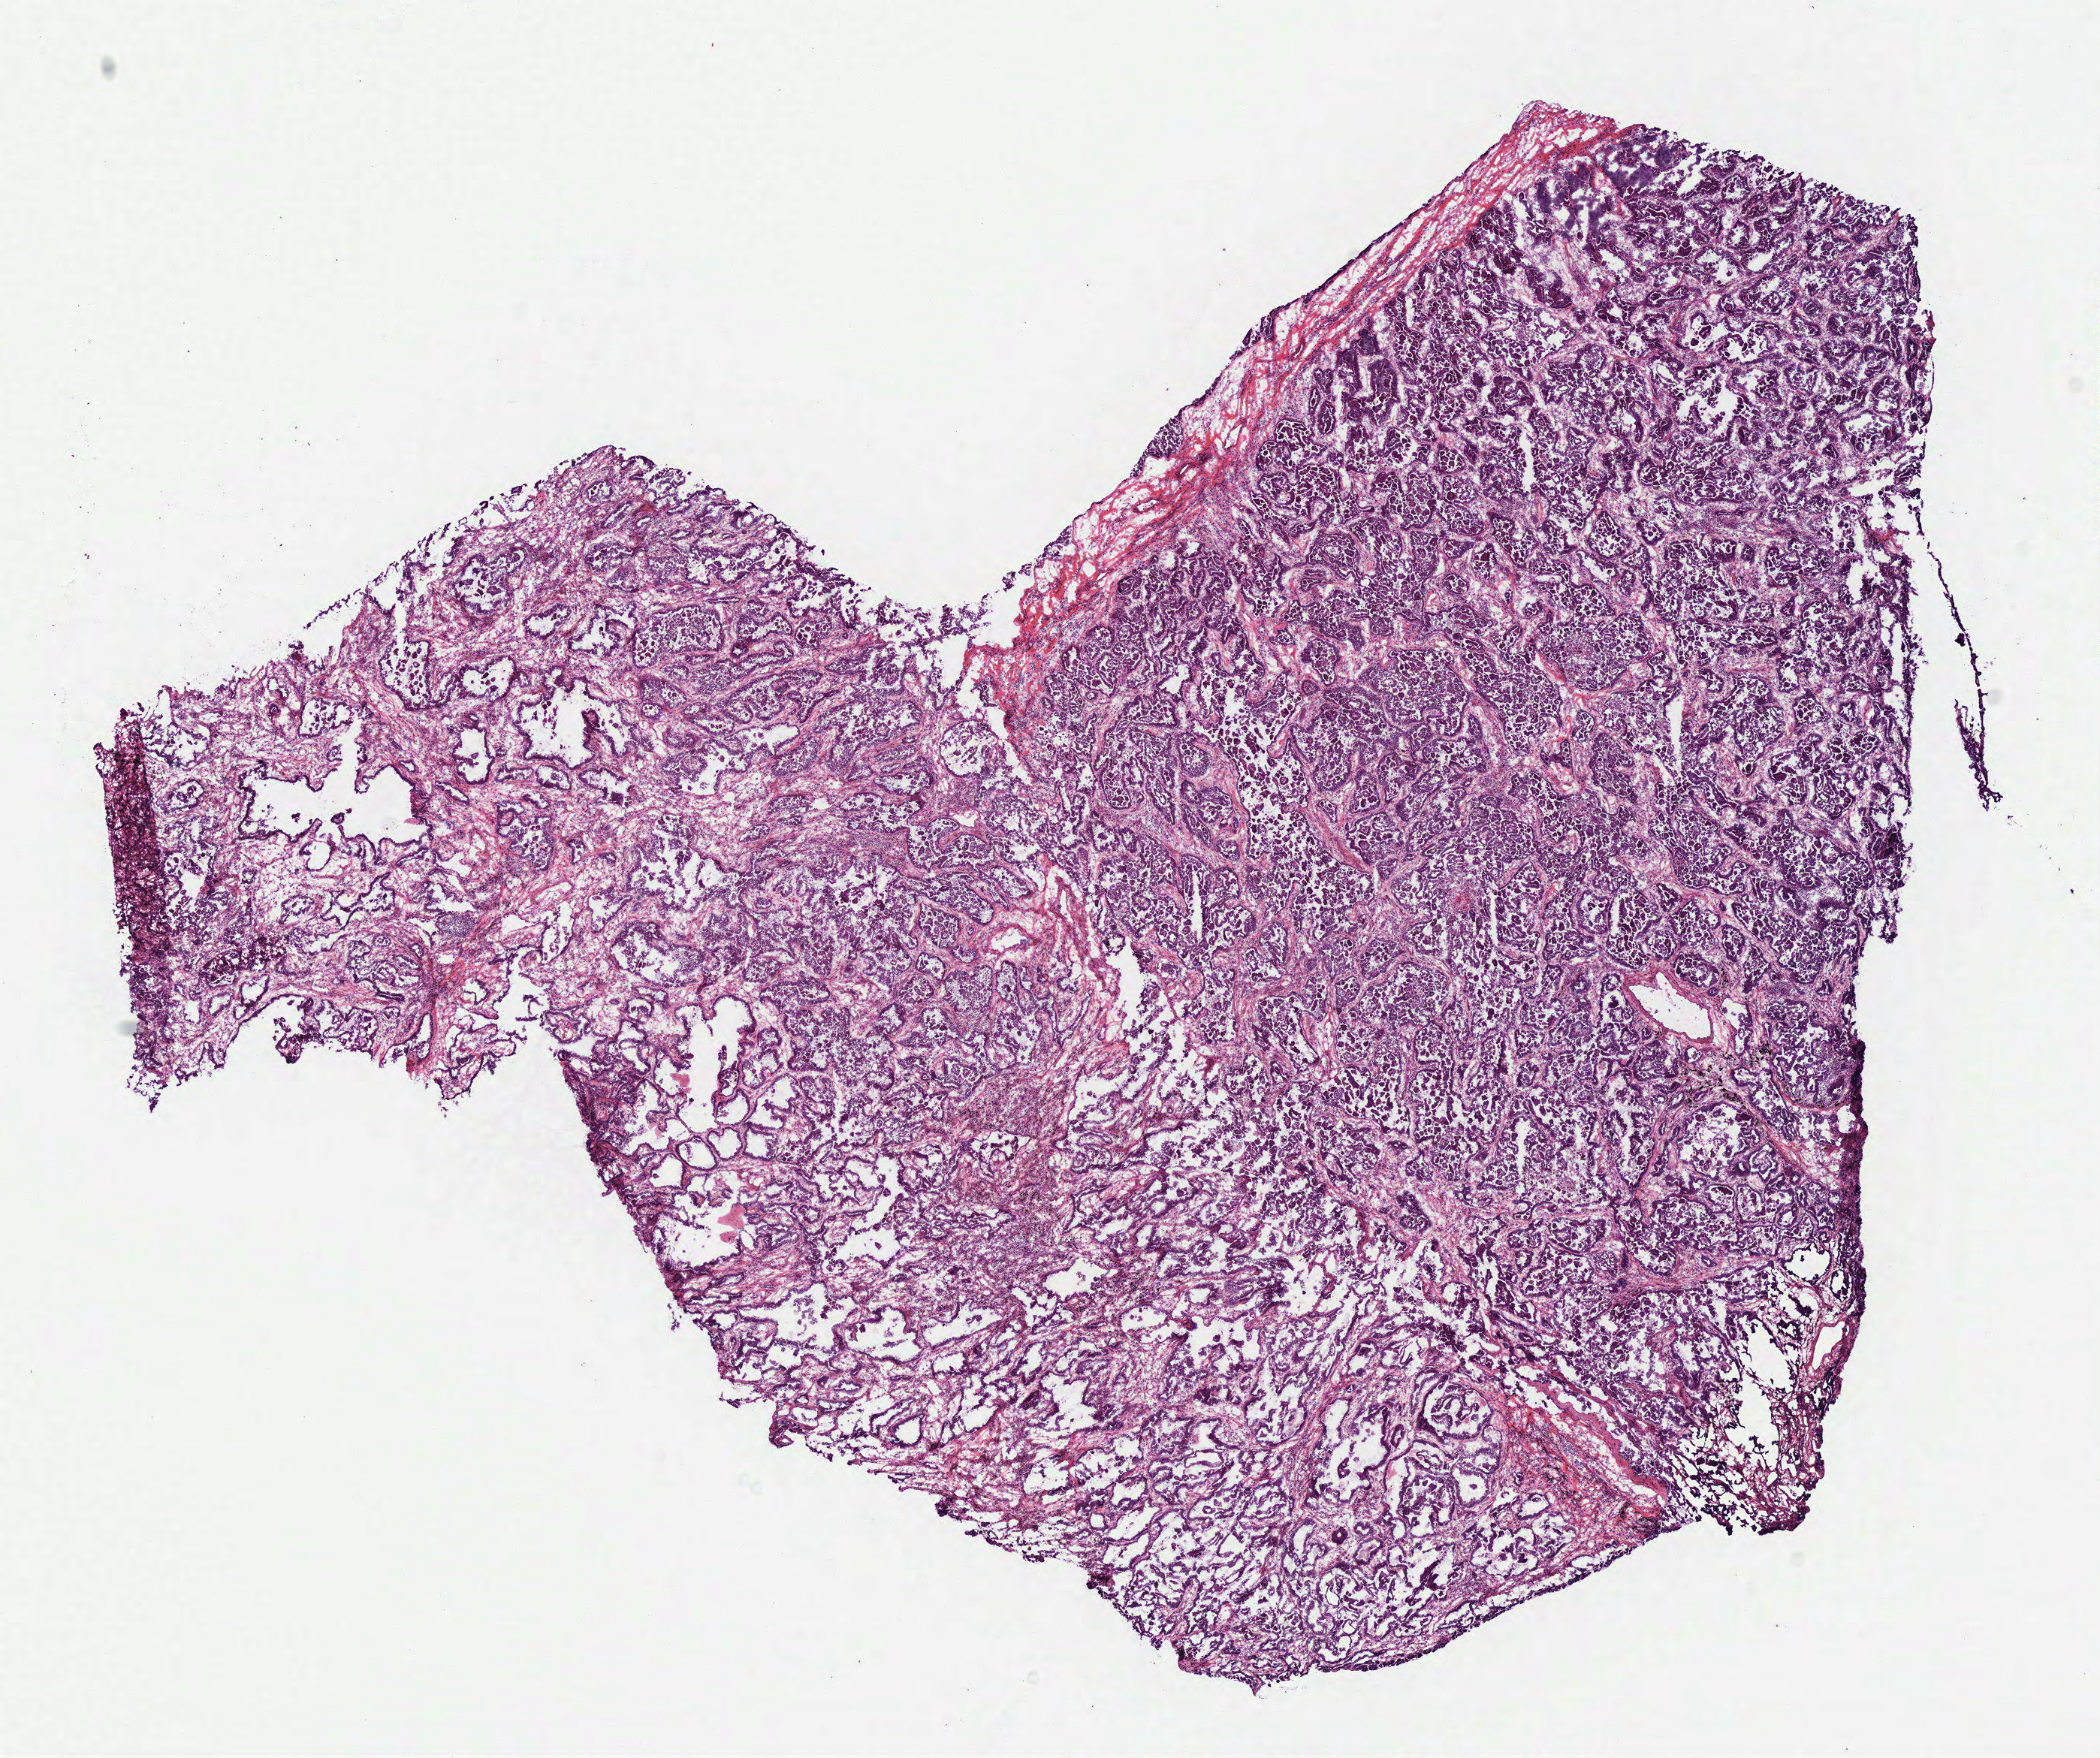
H&E-stained whole-slide image — low-resolution overview of the scanned area, about 11.0 x 9.2 mm (slide scanned at 40x), frozen section from the bottom of the tissue portion, sample: primary tumour, lung. Patient: female, age at initial diagnosis 59 years. Pathologist review of this section (percent, as recorded): tumour cells 85%, tumour nuclei 70%, normal cells 0%, stromal cells 15%, necrosis 0%.
* AJCC pathologic stage: IIIB (6th edition)
* laterality: left
* histologic diagnosis: Adenocarcinoma with mixed subtypes (lower lobe, lung)